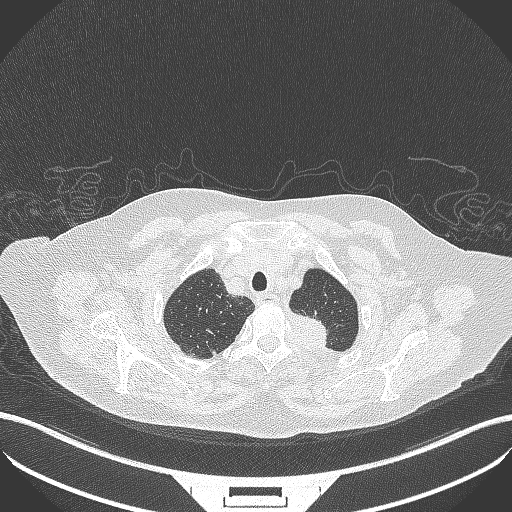
Chest CT, one axial slice; reconstruction kernel B70f; lung window (W 1500 / L -600 HU); 1 mm slice thickness; 512 × 512 image matrix. Patient: female, 81 years. Case-level facts recorded for this patient, not image findings: clinical TNM (as recorded): T2a N0 M0.
Structures marked on this image (bounding box drawn by a radiologist):
- lung tumour (recorded histology: adenocarcinoma): box from (x=284, y=311) to (x=332, y=350) px